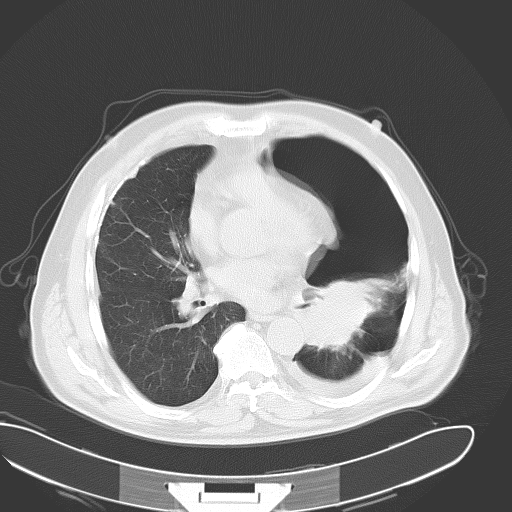
Chest CT, one axial slice; position 22 of 43 along the scan axis; reconstruction kernel B70f; lung window (W 1500 / L -600 HU); 512 × 512 image matrix, field of view 418 × 418 mm. Male patient, age 62 years. From the clinical record (not read from this slice): clinical TNM (as recorded): T3 N0 M1.
Structures marked on this image (bounding box drawn by a radiologist):
- lung tumour (recorded histology: adenocarcinoma): bounding box <299,281,381,355> (left, top, right, bottom; pixels)
- lung tumour (recorded histology: adenocarcinoma): <299,288,386,348>